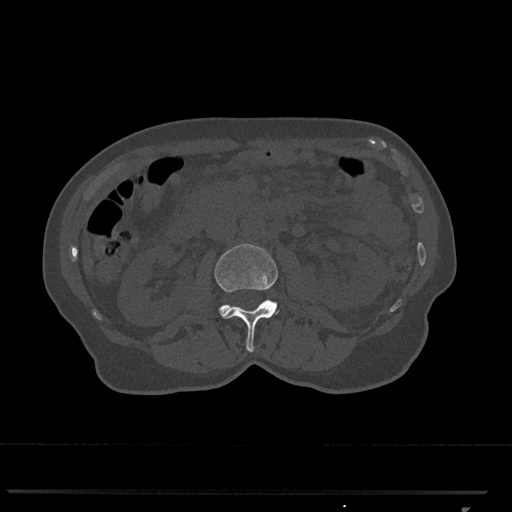
CT including the spine, one axial slice. Slice 329 of 793 in the series (ordered by position). Reconstruction kernel Br40s/3. Bone window (W 1800 / L 400 HU). 512 × 512 image matrix. Patient: female, 62 years. Case-level facts recorded for this patient, not image findings: primary cancer: renal.
Structures marked on this image (semi-automatic segmentation, software-assisted and operator-edited):
- L2 vertebra: bounding box (x1, y1, x2, y2) in pixels: (214, 244, 279, 352)